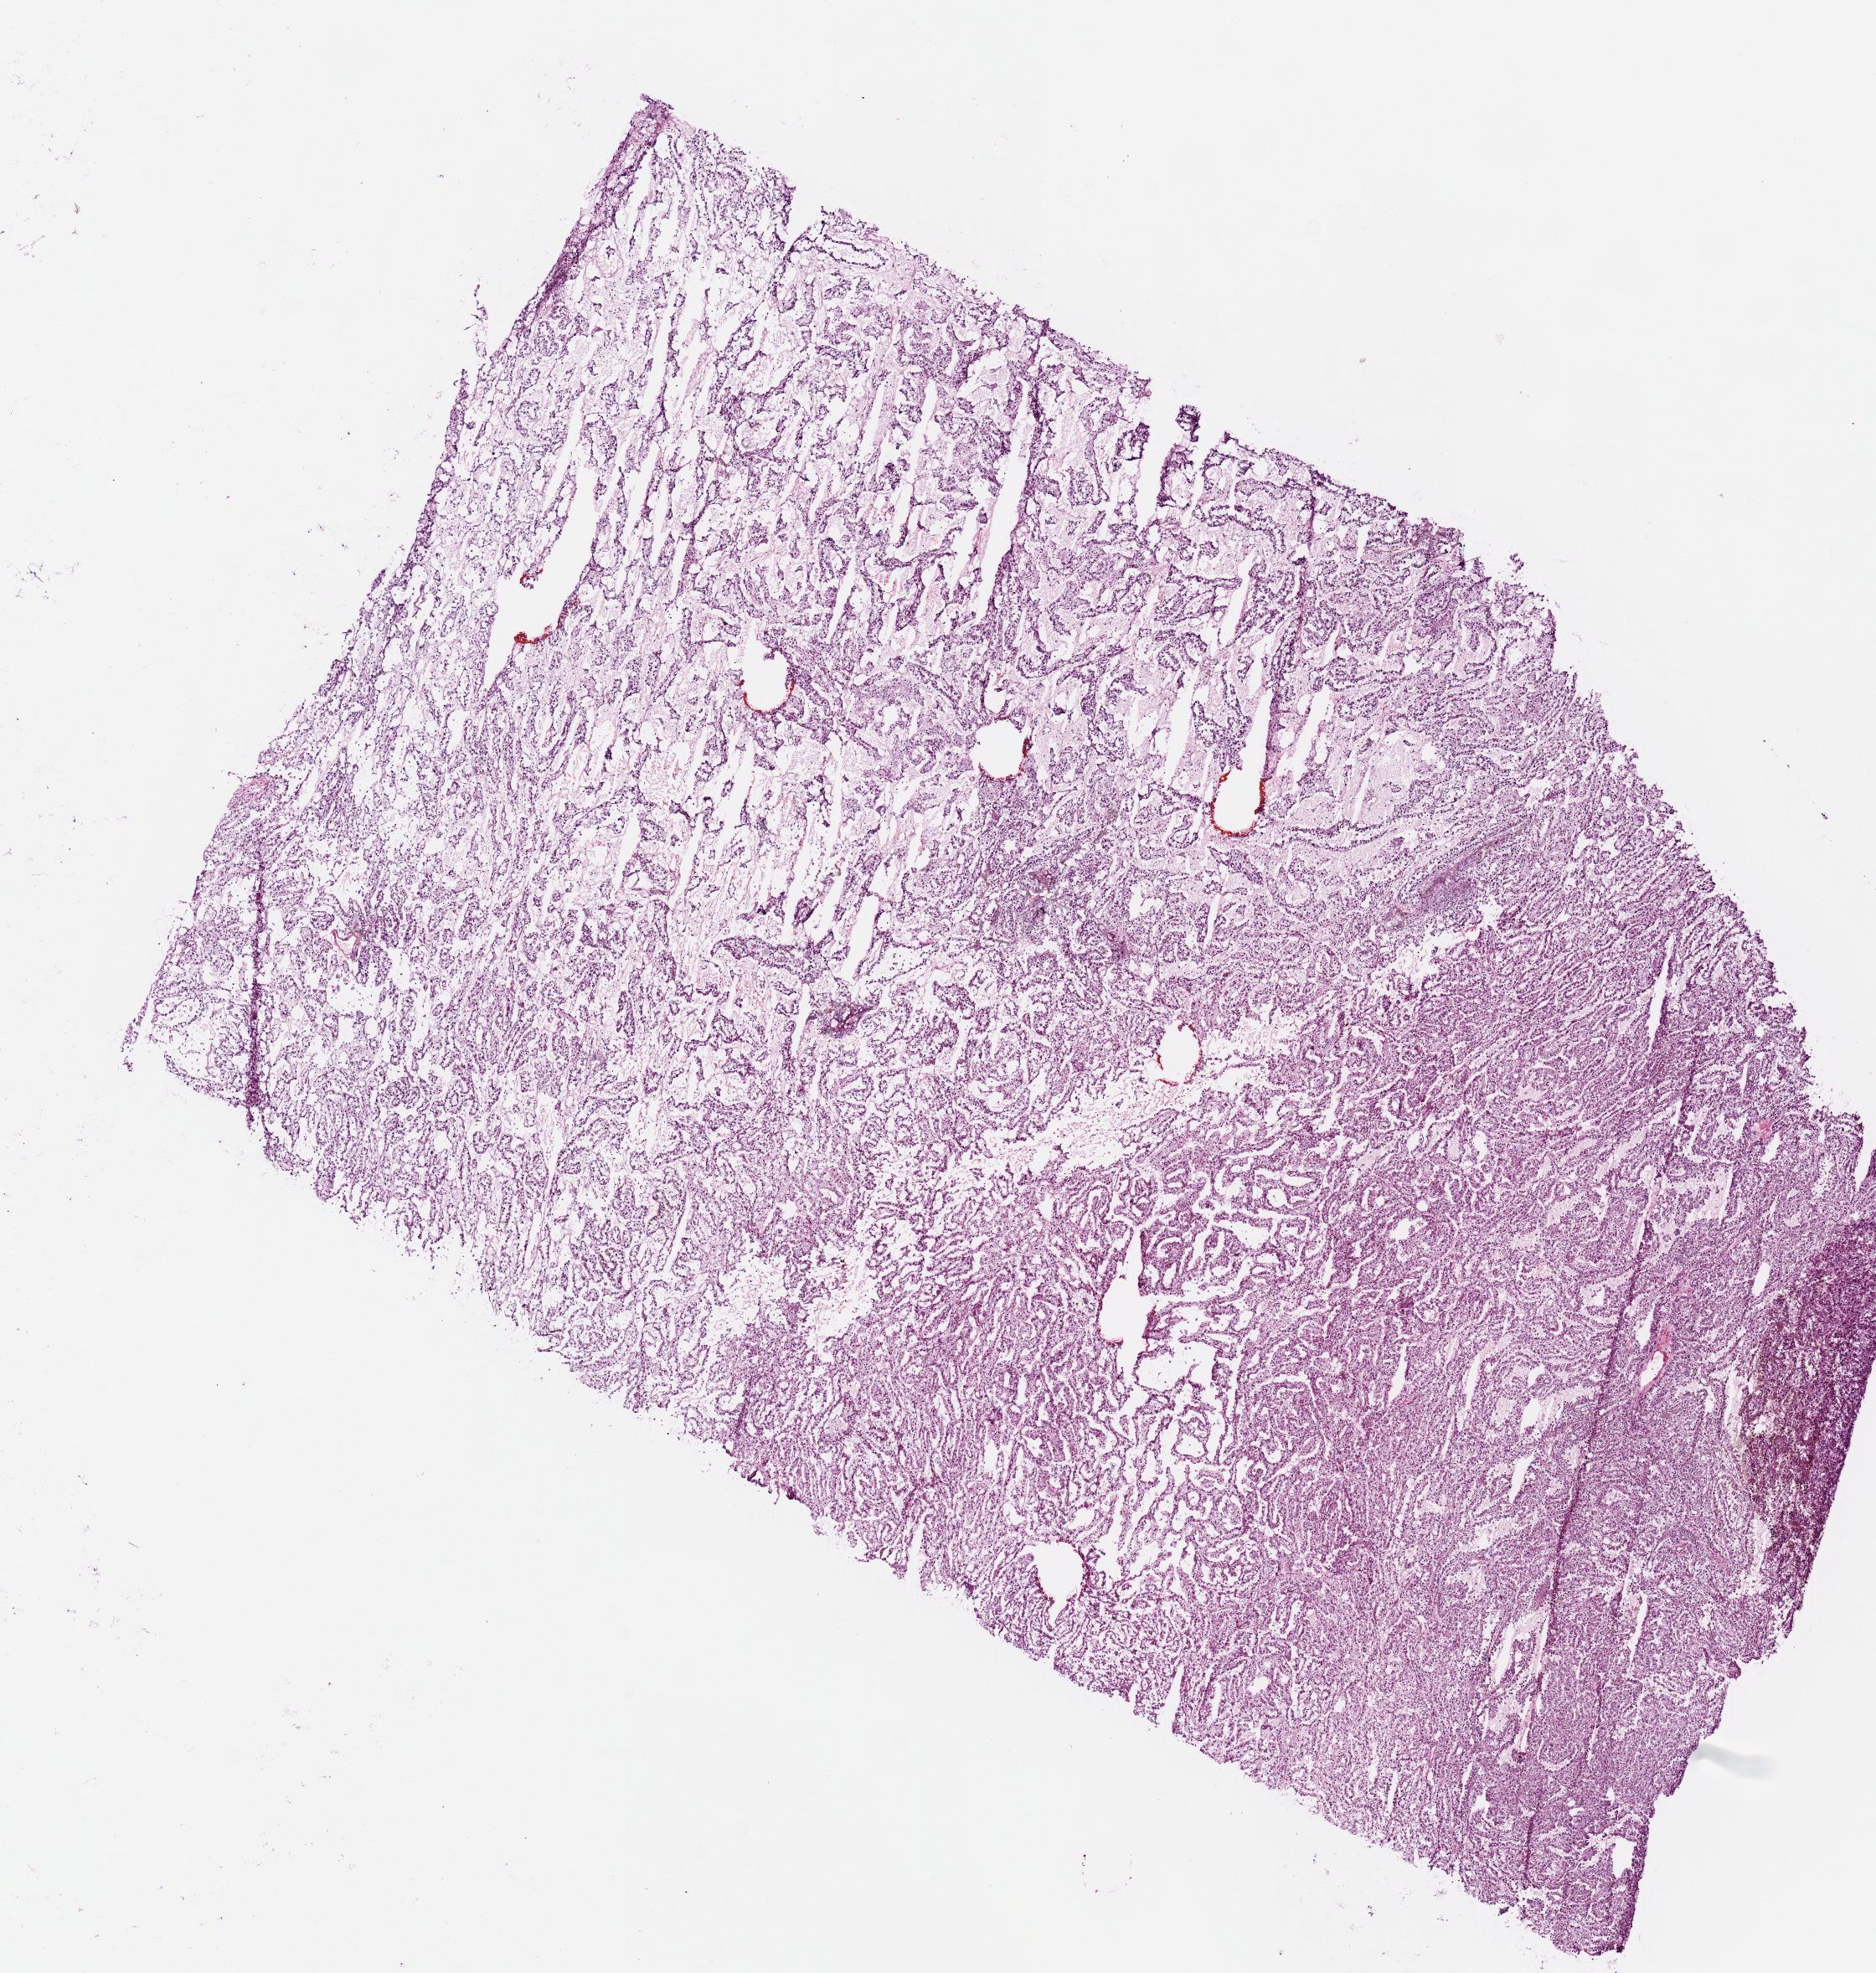
Digitized H&E-stained tissue section (whole slide), shown as a low-resolution overview of the whole scanned area (about 8.9 x 9.3 mm, from a 20x scan), frozen section from the top of the tissue portion, kidney, primary tumour sample. Female patient; age at initial diagnosis 59 years. Slide review estimates, as recorded: tumour nuclei 85%, necrosis 0%.
Laterality: right. AJCC pathologic stage: I. Diagnosis: Papillary adenocarcinoma, NOS.